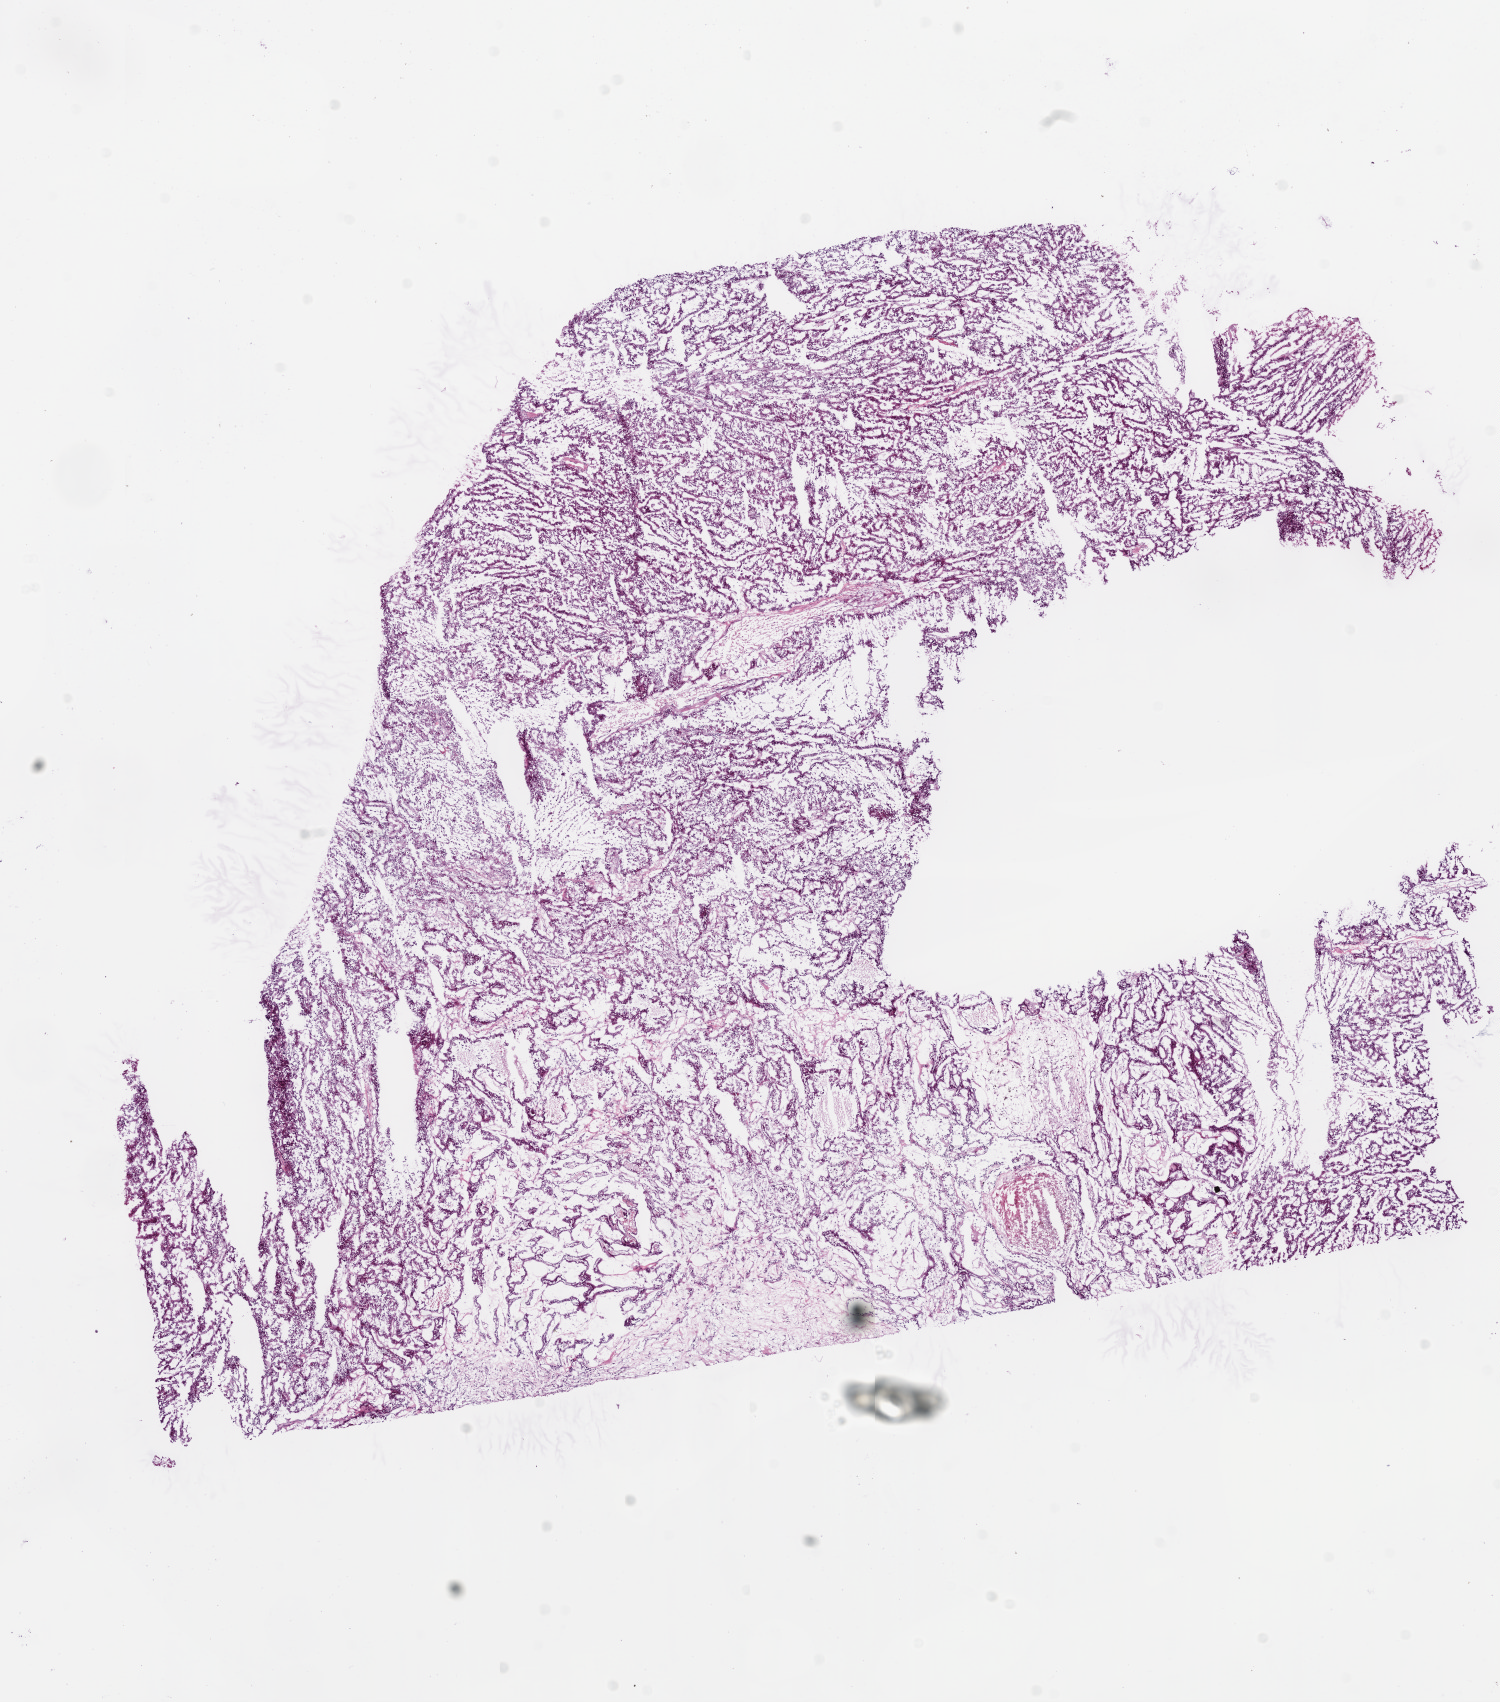
H&E whole-slide image — shown as a low-resolution overview of the whole scanned area (about 12.0 x 13.7 mm, slide scanned at 20x), frozen section, primary tumour sample from the kidney. Male, age 48 years at initial diagnosis. Histologic grade: G3 (poorly differentiated). Pathologist review of this section (percent, as recorded): tumour cells 75%, tumour nuclei 76%, normal cells 10%, stromal cells 0%, necrosis 15%.
- TNM: T2 N0 M0
- lymph nodes positive (case pathology): 0 of 1 examined
- diagnosis: Clear cell adenocarcinoma, NOS
- AJCC pathologic stage: II